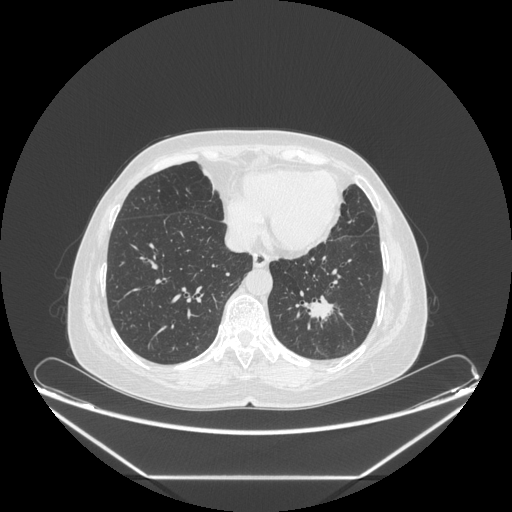
Chest CT, one axial slice. Position 78 of 241 along the scan axis. Reconstruction kernel STANDARD. 120 kVp. Lung window (W 1500 / L -600 HU). 1.25 mm slice thickness. 512 × 512 image matrix, field of view 451 × 451 mm. Female patient, age 63 years. From the clinical record (not read from this slice): clinical TNM (as recorded): T1c N0 M0; histopathological grade: G2-3.
Outlined on this slice (bounding box drawn by a radiologist):
- lung tumour (recorded histology: adenocarcinoma): bounding box [x1, y1, x2, y2] px = [298, 293, 351, 338]